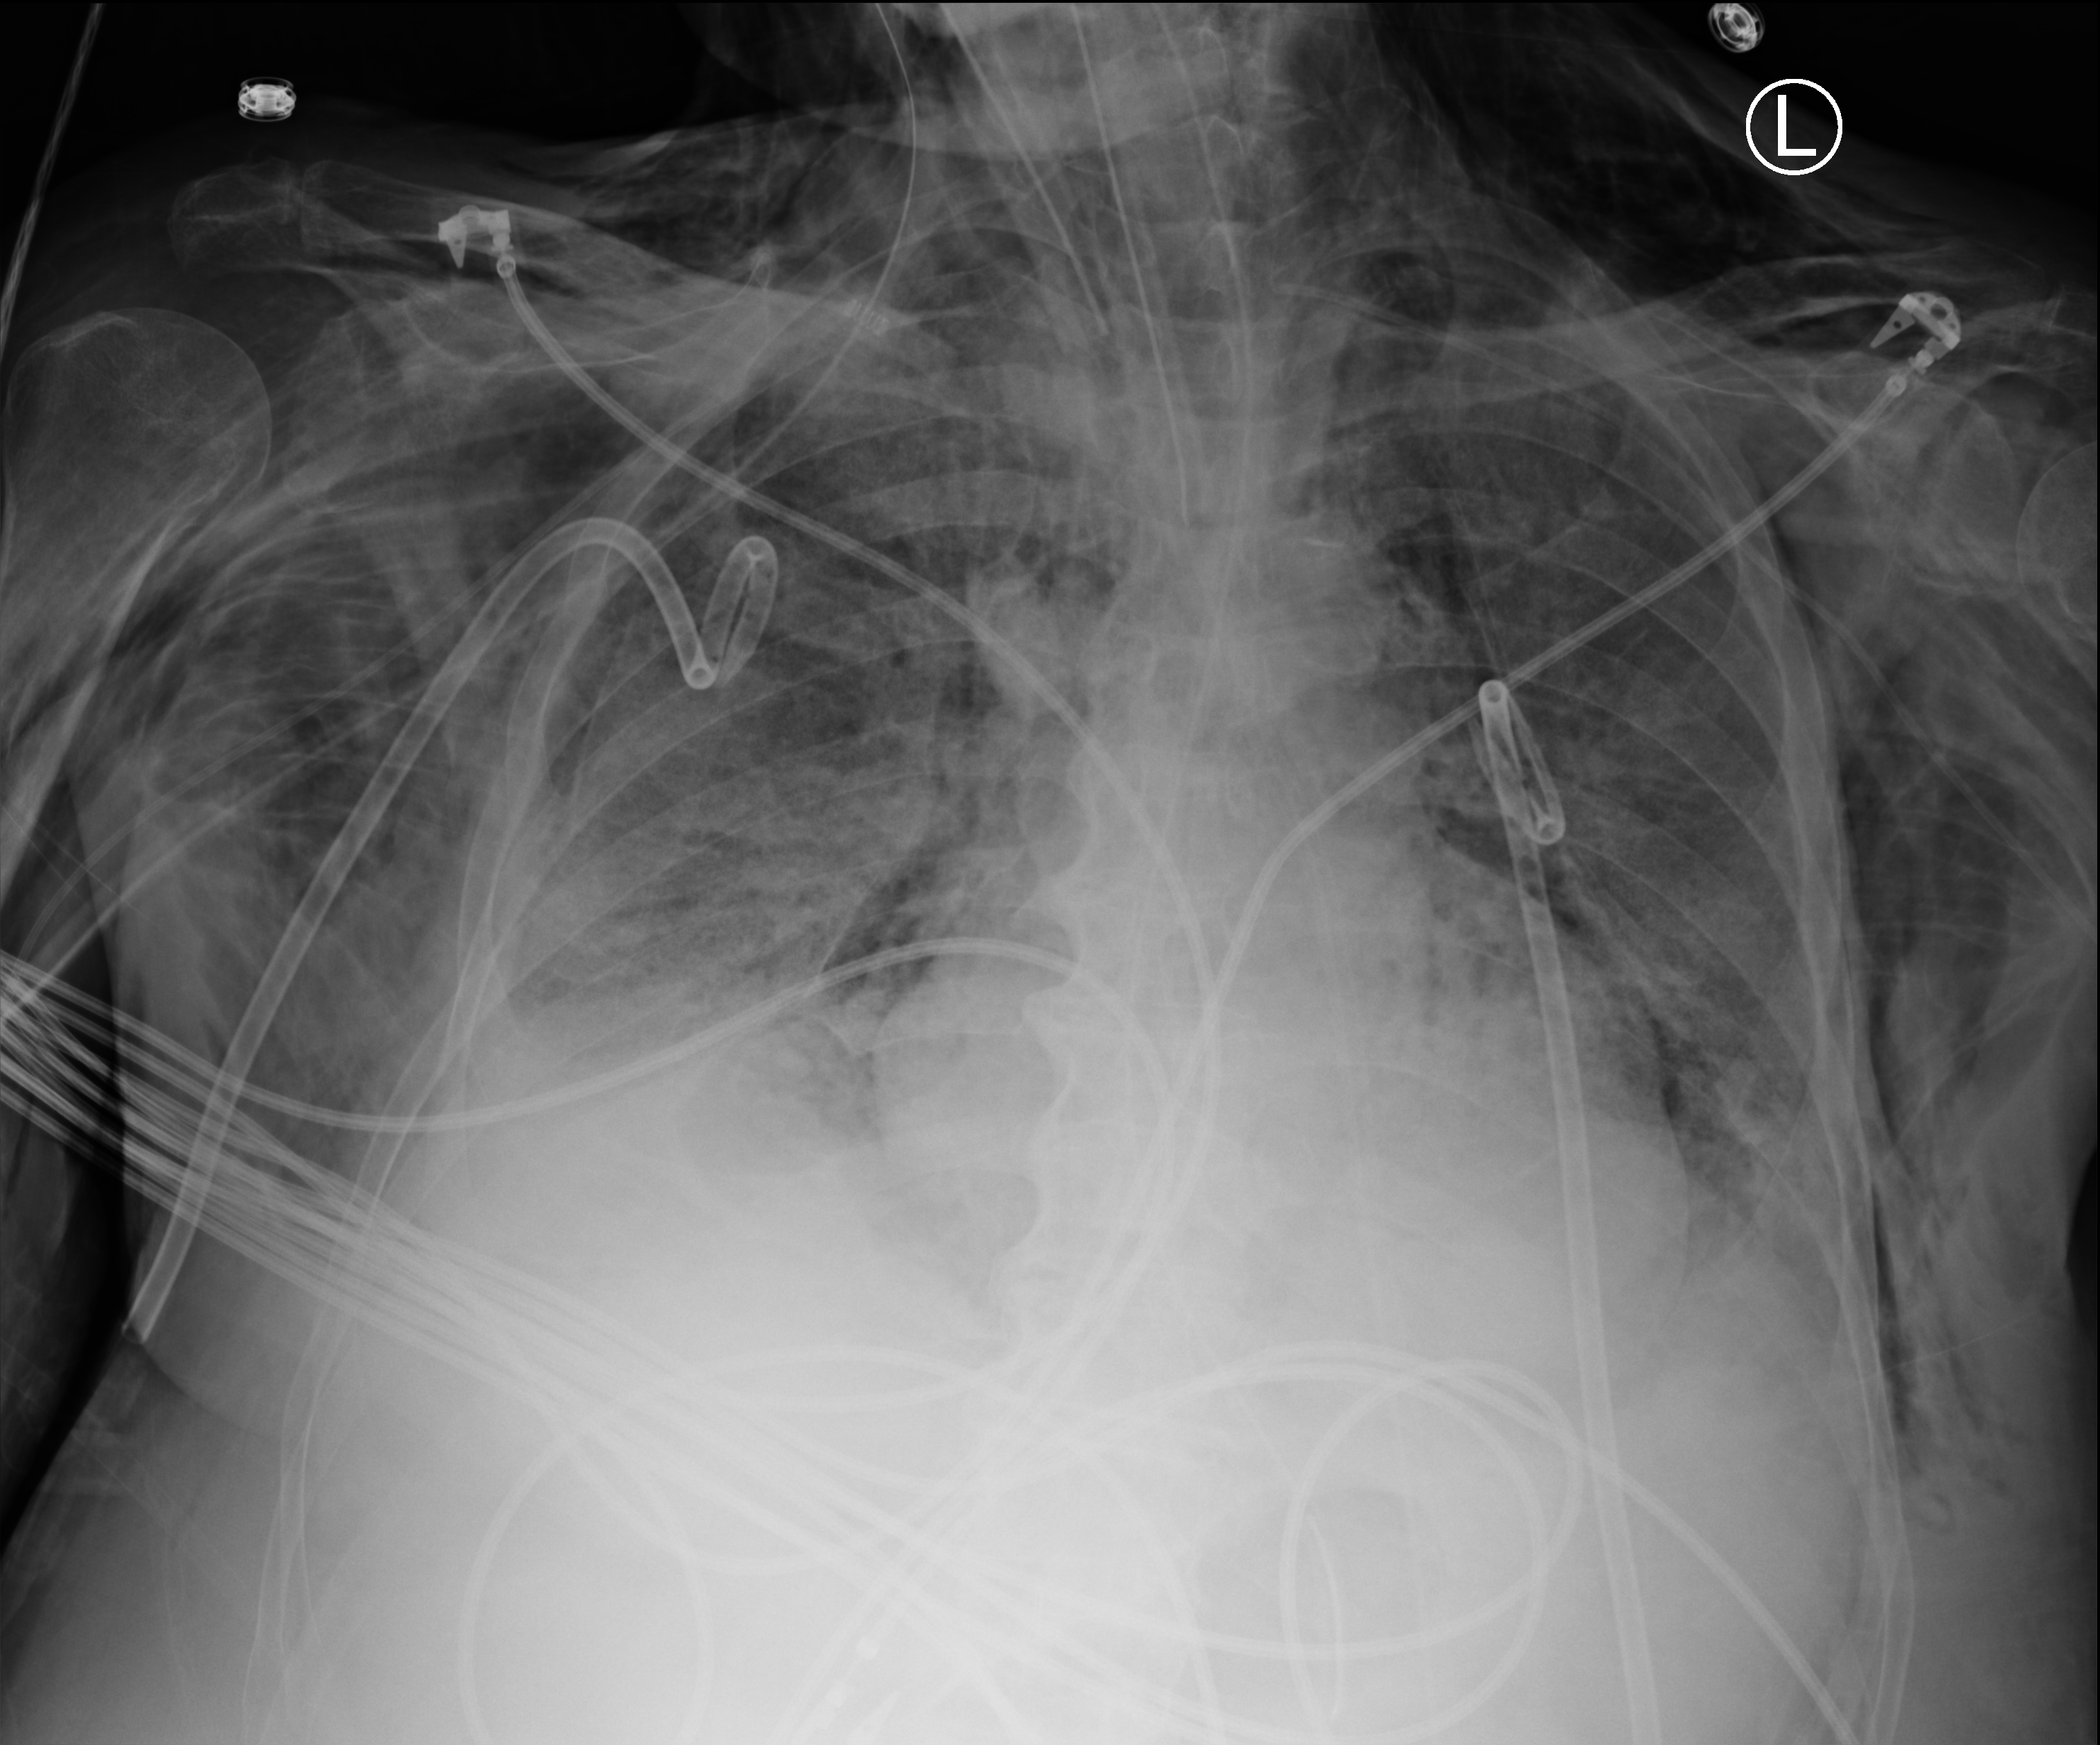
Portable chest radiograph; anteroposterior (AP) projection. Patient hospitalised with COVID-19; male, aged 75–90 years.
From the hospital-stay record, not from the radiograph (when in the stay this image was taken is not recorded): hypertension (admission record): yes; admitted to intensive care during this hospital stay: yes.